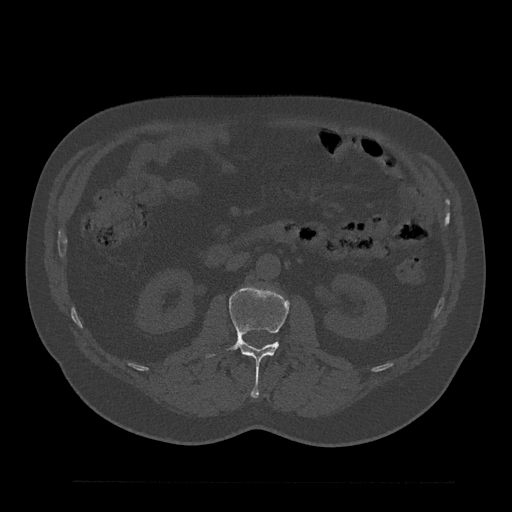
CT including the spine, one axial slice. Slice 95 of 797 in the series (ordered by position). Reconstruction kernel Br40s/3. 120 kVp. Bone window (W 1800 / L 400 HU). 512 × 512 image matrix, field of view 430 × 430 mm. Male patient, age 61 years. Case-level facts recorded for this patient, not image findings: primary cancer: prostate.
Outlined on this slice (semi-automatic segmentation, software-assisted and operator-edited):
- L2 vertebra: box from (x=205, y=285) to (x=312, y=398) px